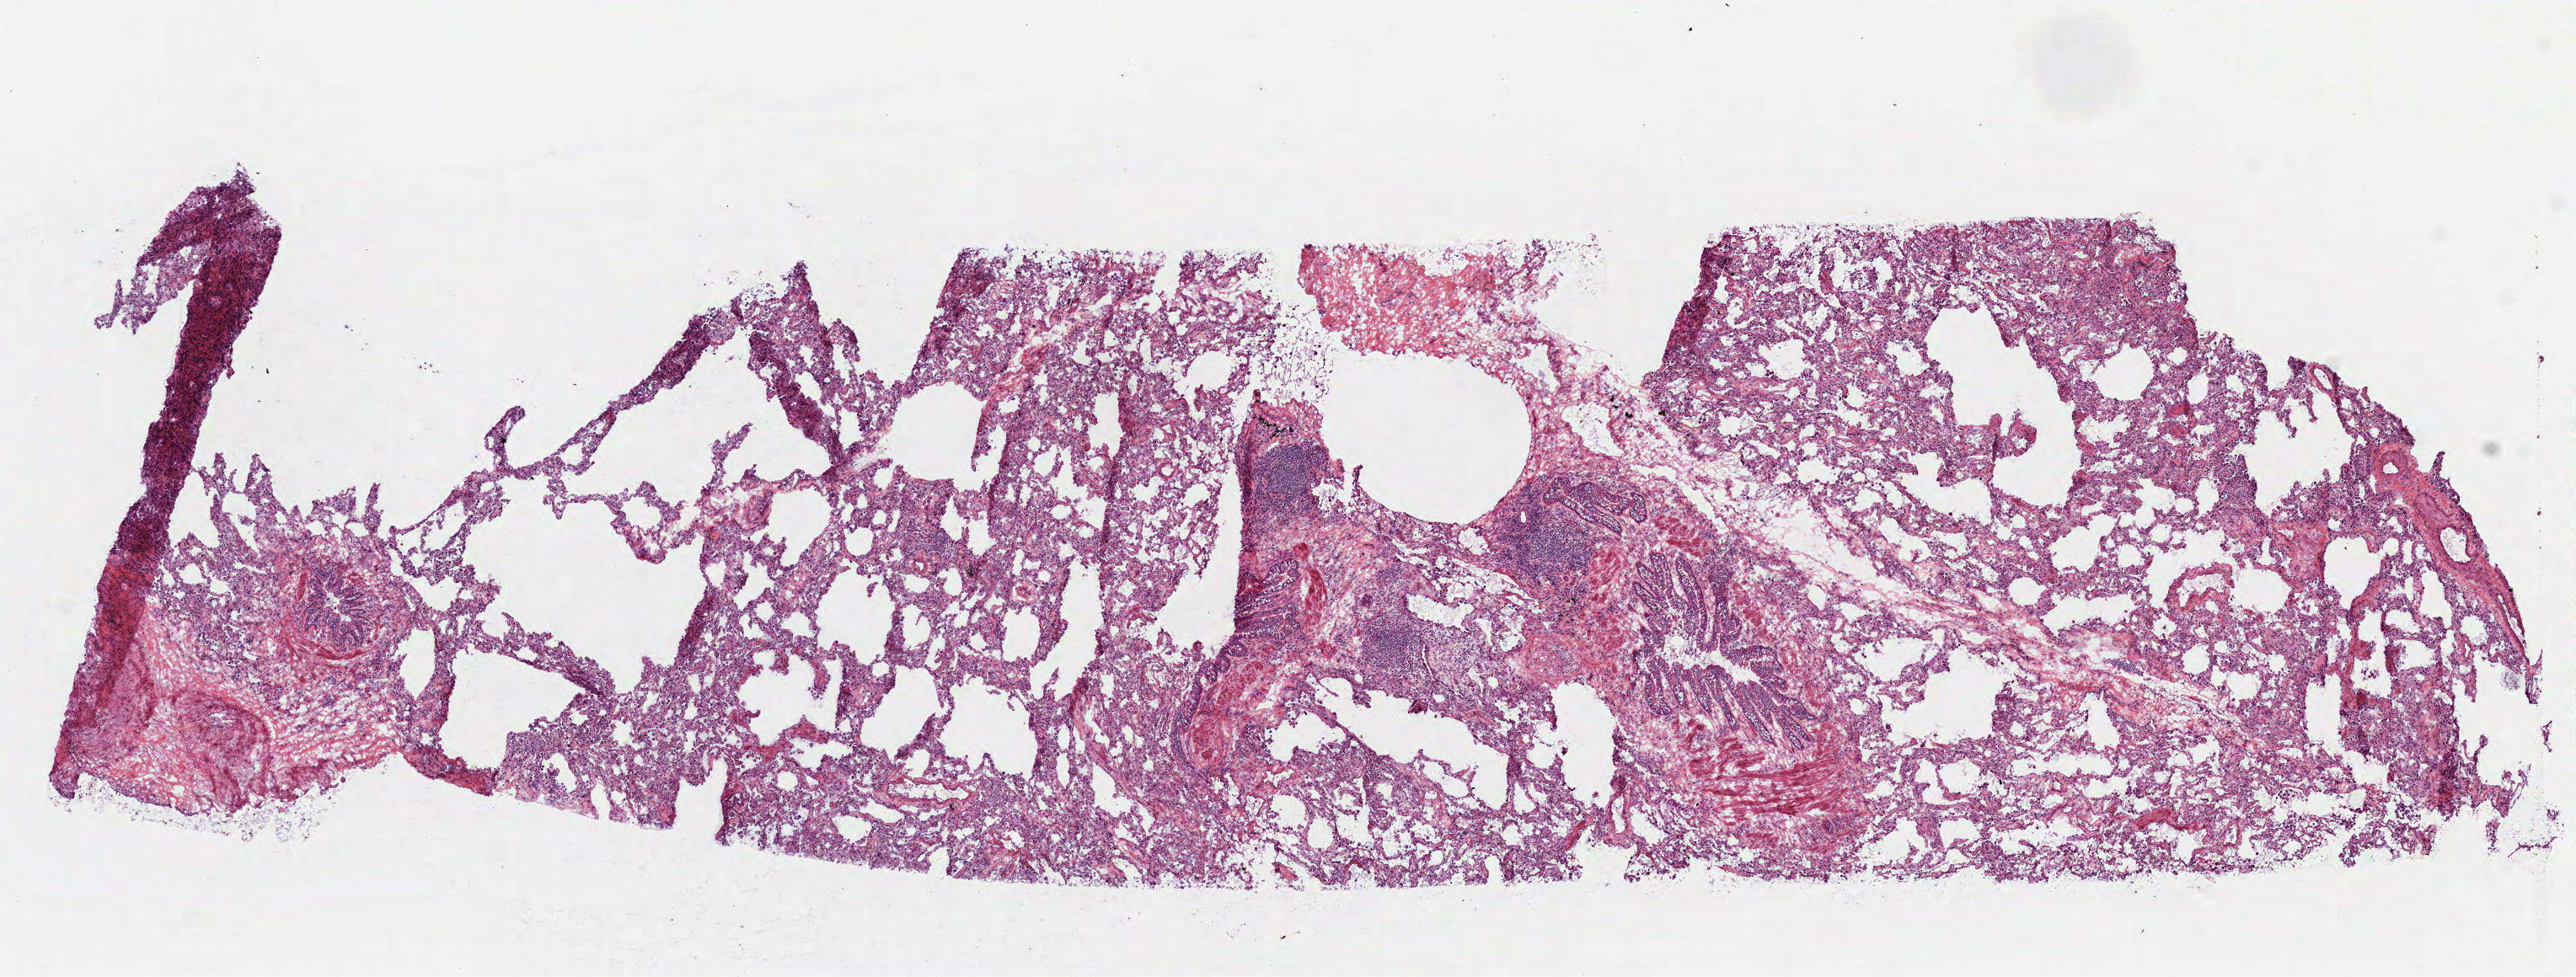
Digitized Hematoxylin and eosin (H&E) stained tissue section (whole slide) — shown as a low-resolution overview of the whole scanned area (about 12.3 x 4.7 mm). Frozen section from the top of the tissue portion. Lung, solid tissue normal (non-tumour tissue) sample. Female patient; age at initial diagnosis 76 years.
This section: solid tissue normal (non-tumour) sample from the same patient. Patient diagnosis: Bronchiolo-alveolar carcinoma, non-mucinous (upper lobe, lung).